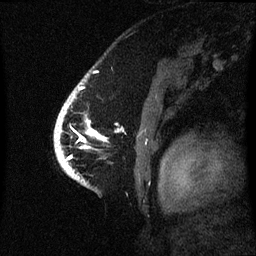
Breast MRI (dynamic contrast-enhanced), one sagittal slice. Position 50 of 60 along the scan axis. Dynamic contrast-enhanced series, image 2 of 3 at this slice position (ordered by acquisition). 1.5 T. TE 4.2 ms, TR 8.4 ms. 2.1 mm slice thickness. 256 × 256 image matrix, field of view 220 × 220 mm. Female patient, age 53 years. Case-level facts recorded for this patient, not image findings: setting: breast cancer imaged before/during neoadjuvant chemotherapy; receptor status: HR-positive, HER2-negative.
Structures marked on this image (semi-automatic segmentation, software-assisted and operator-edited):
- analysis volume of interest (the breast-tissue region the enhancement analysis was run in; not a lesion): bounding box [x1, y1, x2, y2] px = [55, 90, 102, 171]
- tumour enhancement mask (voxels above the 70 % enhancement threshold inside the analysis volume of interest): [57, 124, 101, 169]